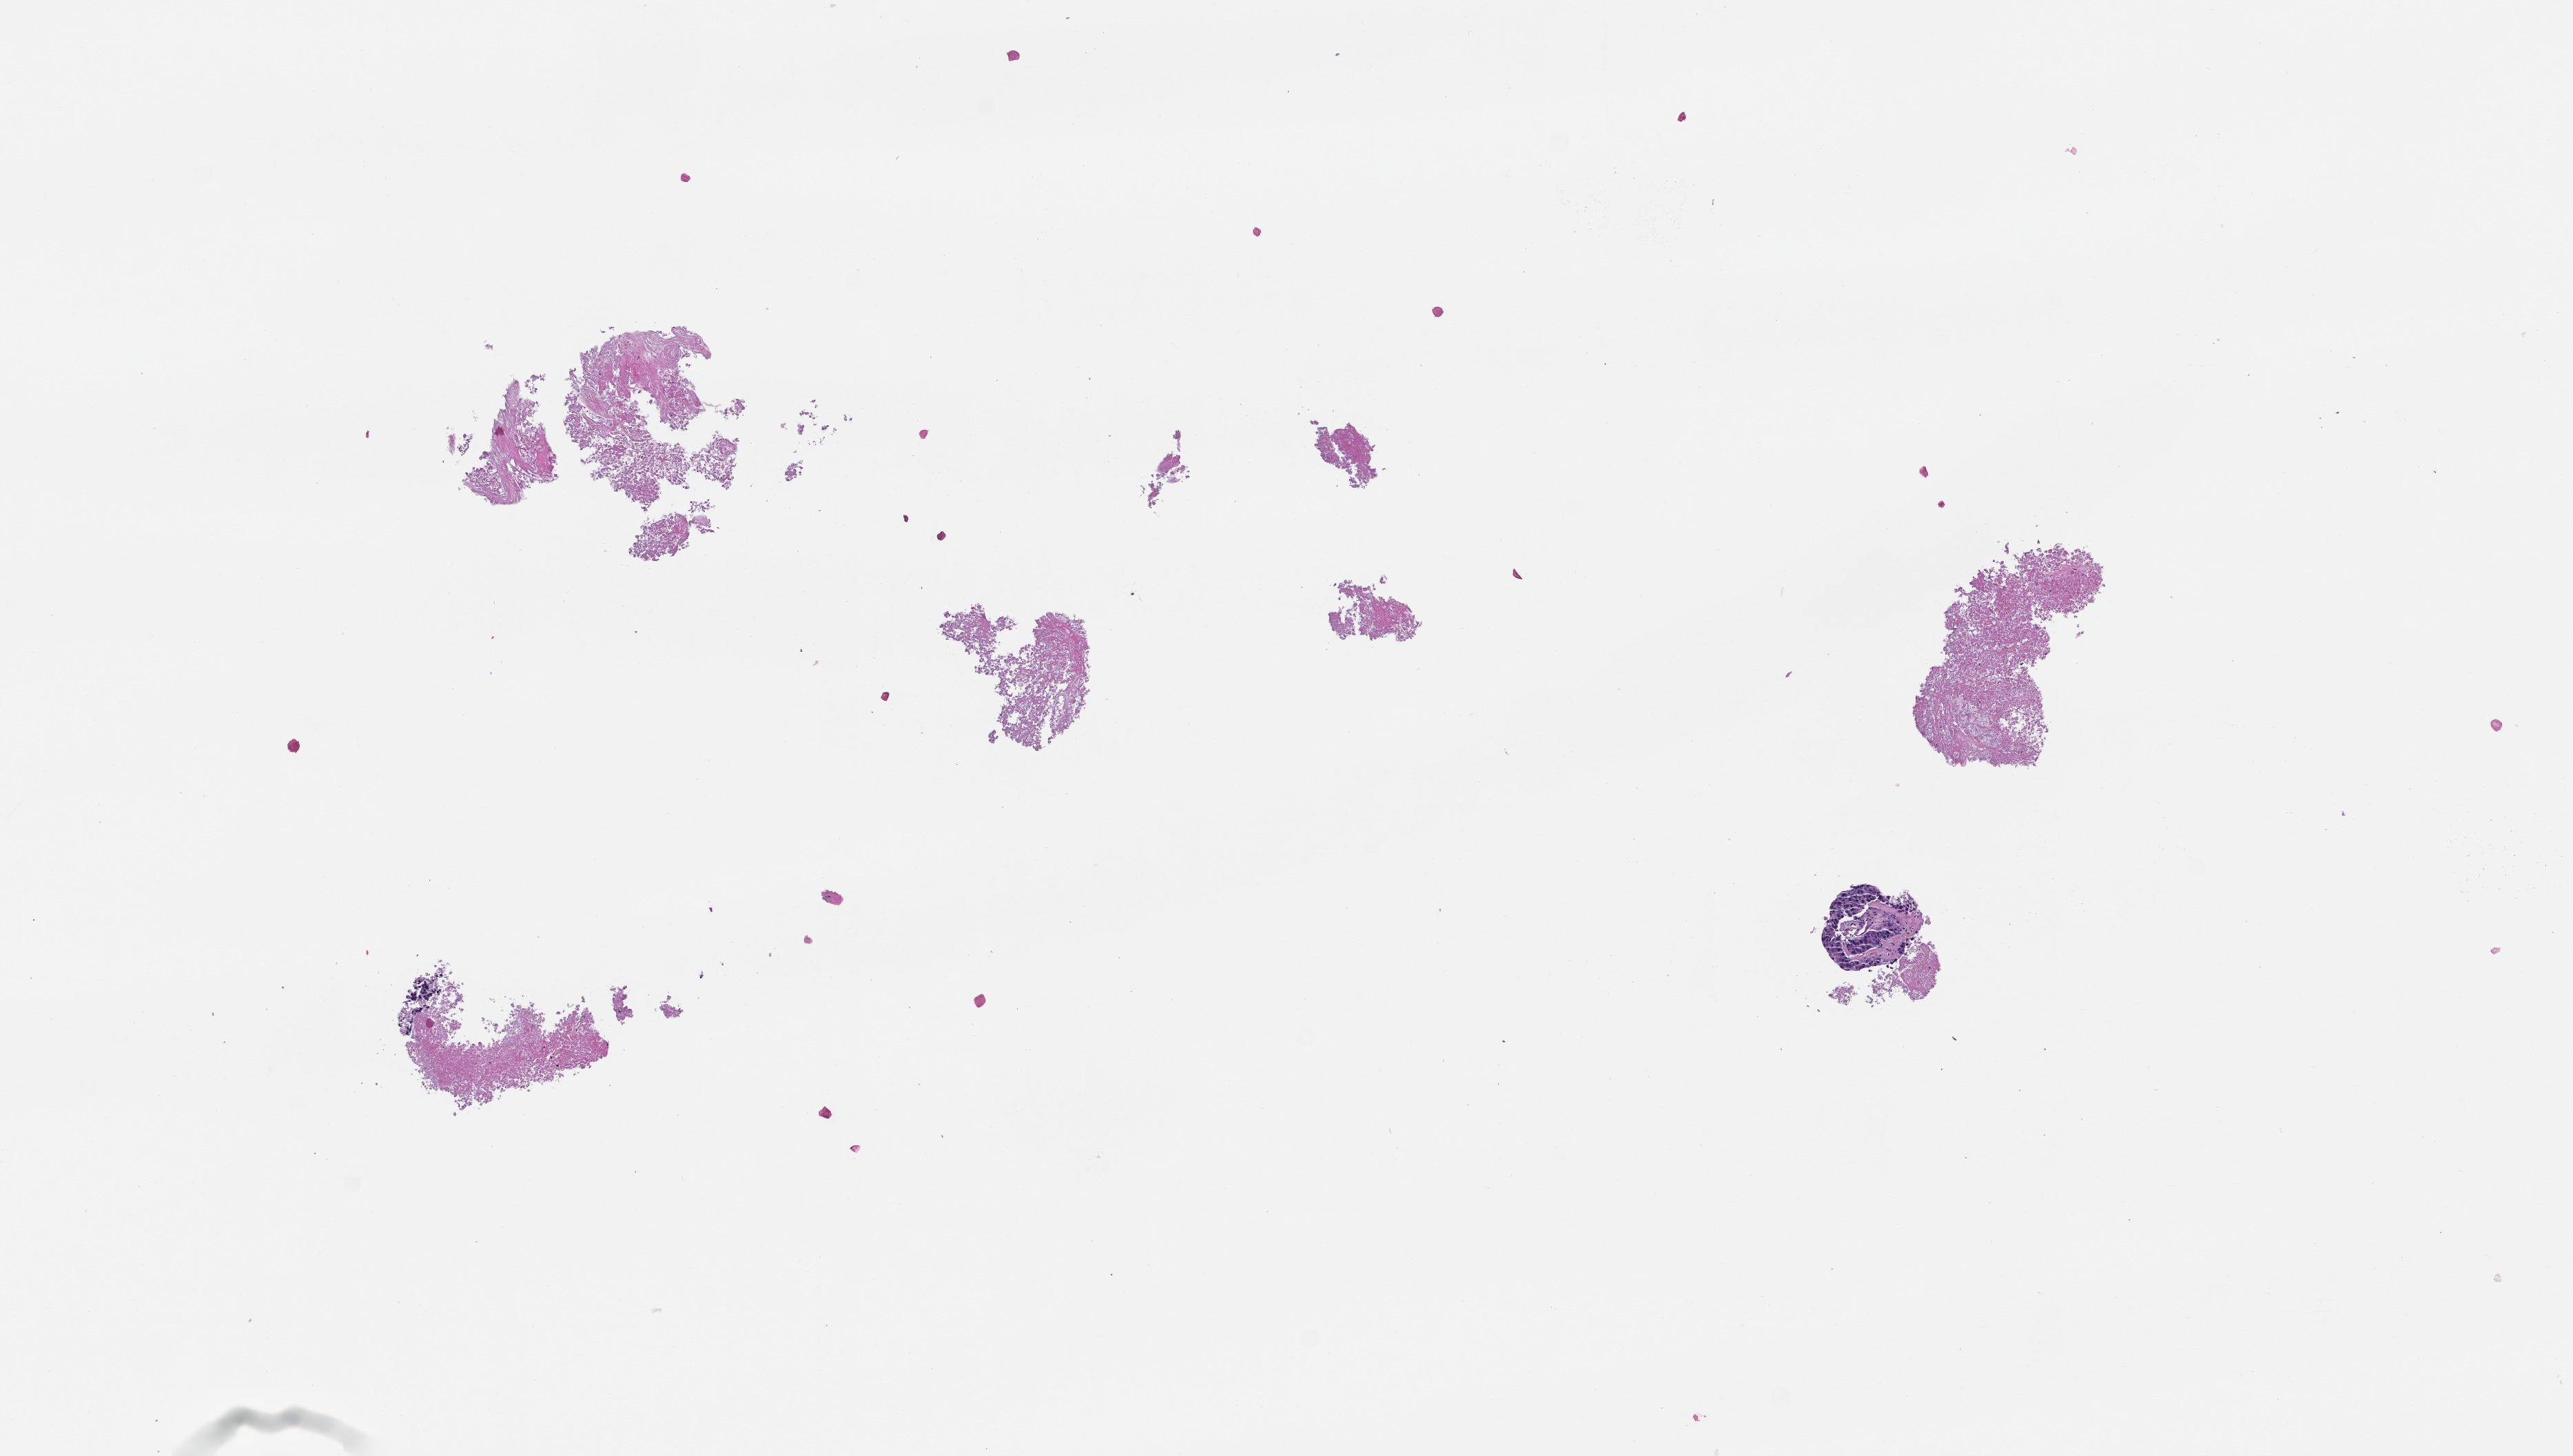
Whole-slide image, hematoxylin and eosin (H&E) stain — a low-resolution overview of the entire scanned area, about 7.5 x 4.3 mm; formalin-fixed paraffin-embedded section; specimen time point: collected at baseline (before treatment). Patient sex: female.
This section: metastasis (sampled organ not recorded). Primary diagnosis of the patient: Colorectal Carcinoma.